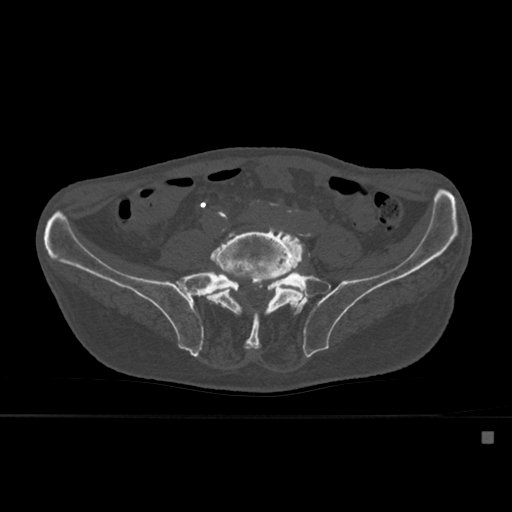
CT including the spine, one axial slice. Position 171 of 527 along the scan axis. Bone window (W 1800 / L 400 HU). 1.5 mm slice thickness. 512 × 512 image matrix. Male patient, age 78 years. Case-level facts recorded for this patient, not image findings: primary cancer: prostate.
Structures marked on this image (semi-automatic segmentation, software-assisted and operator-edited):
- L5 vertebra: bounding box <207,227,306,350> (left, top, right, bottom; pixels)